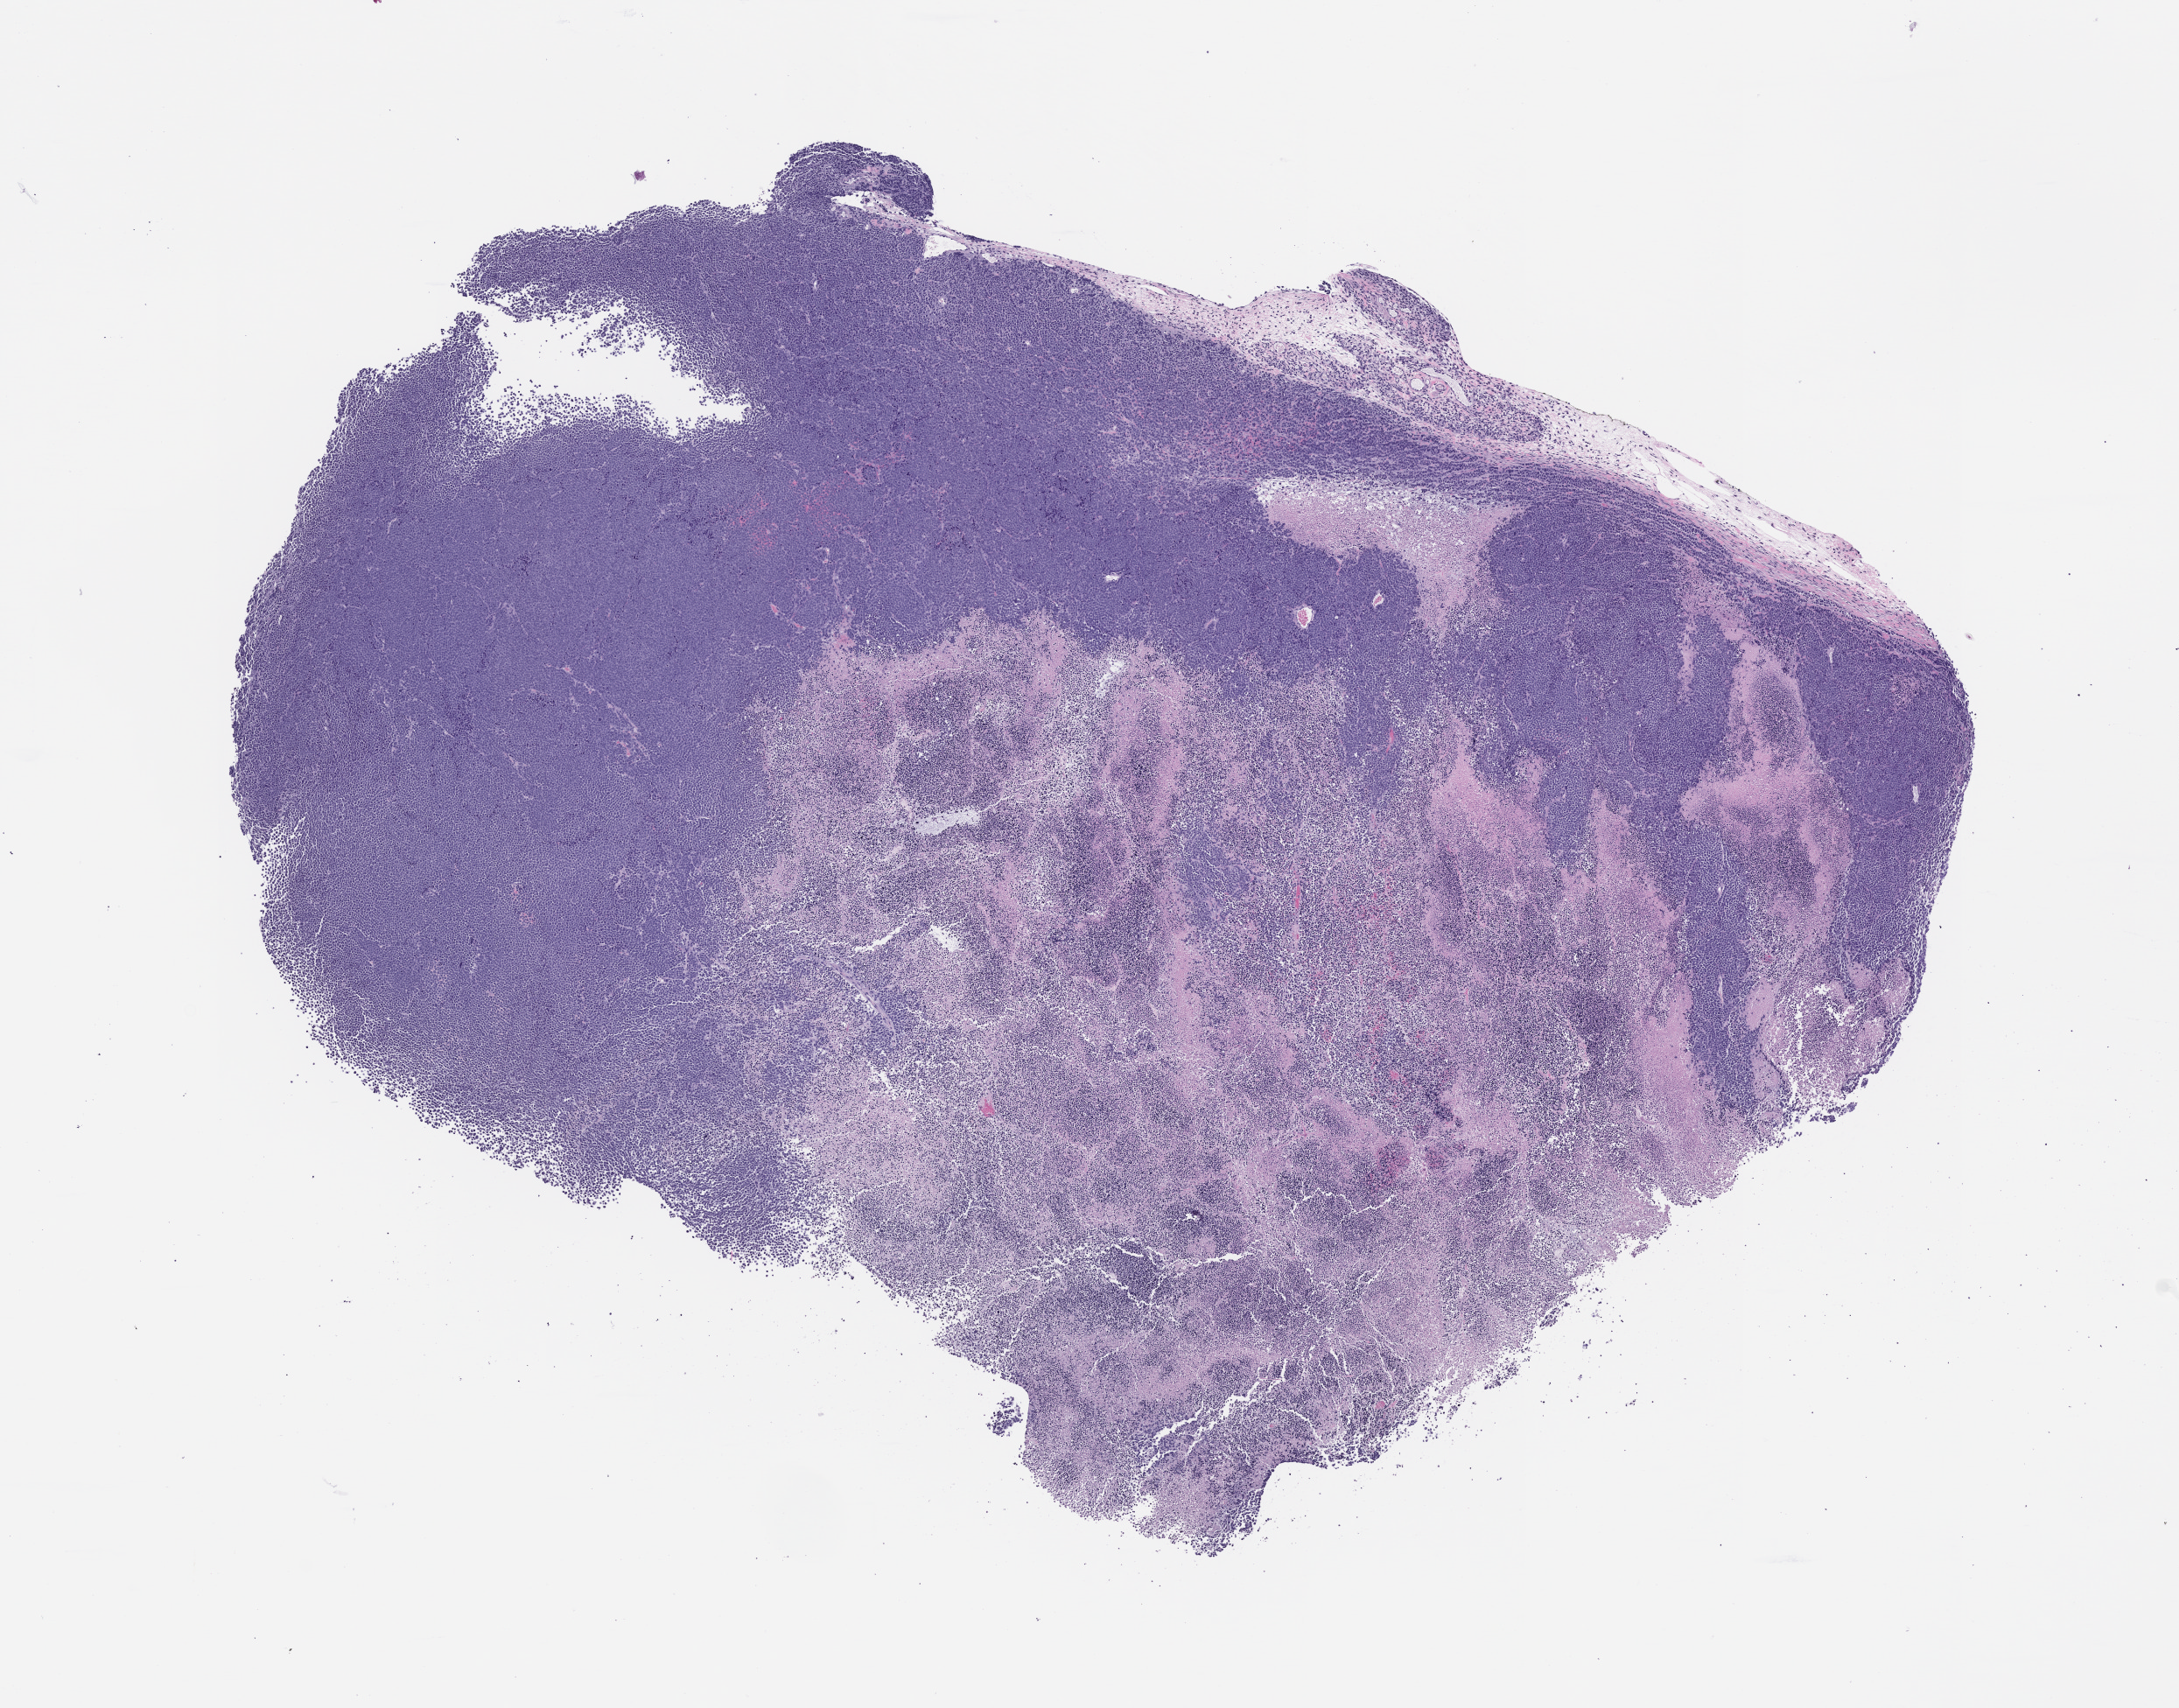
Hematoxylin and eosin (H&E) whole-slide image of a patient-derived xenograft (PDX) tumor grown in a mouse, passage 1 — shown as a low-resolution overview of the whole scanned area (about 10.0 x 7.9 mm), formalin-fixed paraffin-embedded section, tumor site category: endocrine.
Originating patient diagnosis: Merkel Cell Carcinoma.